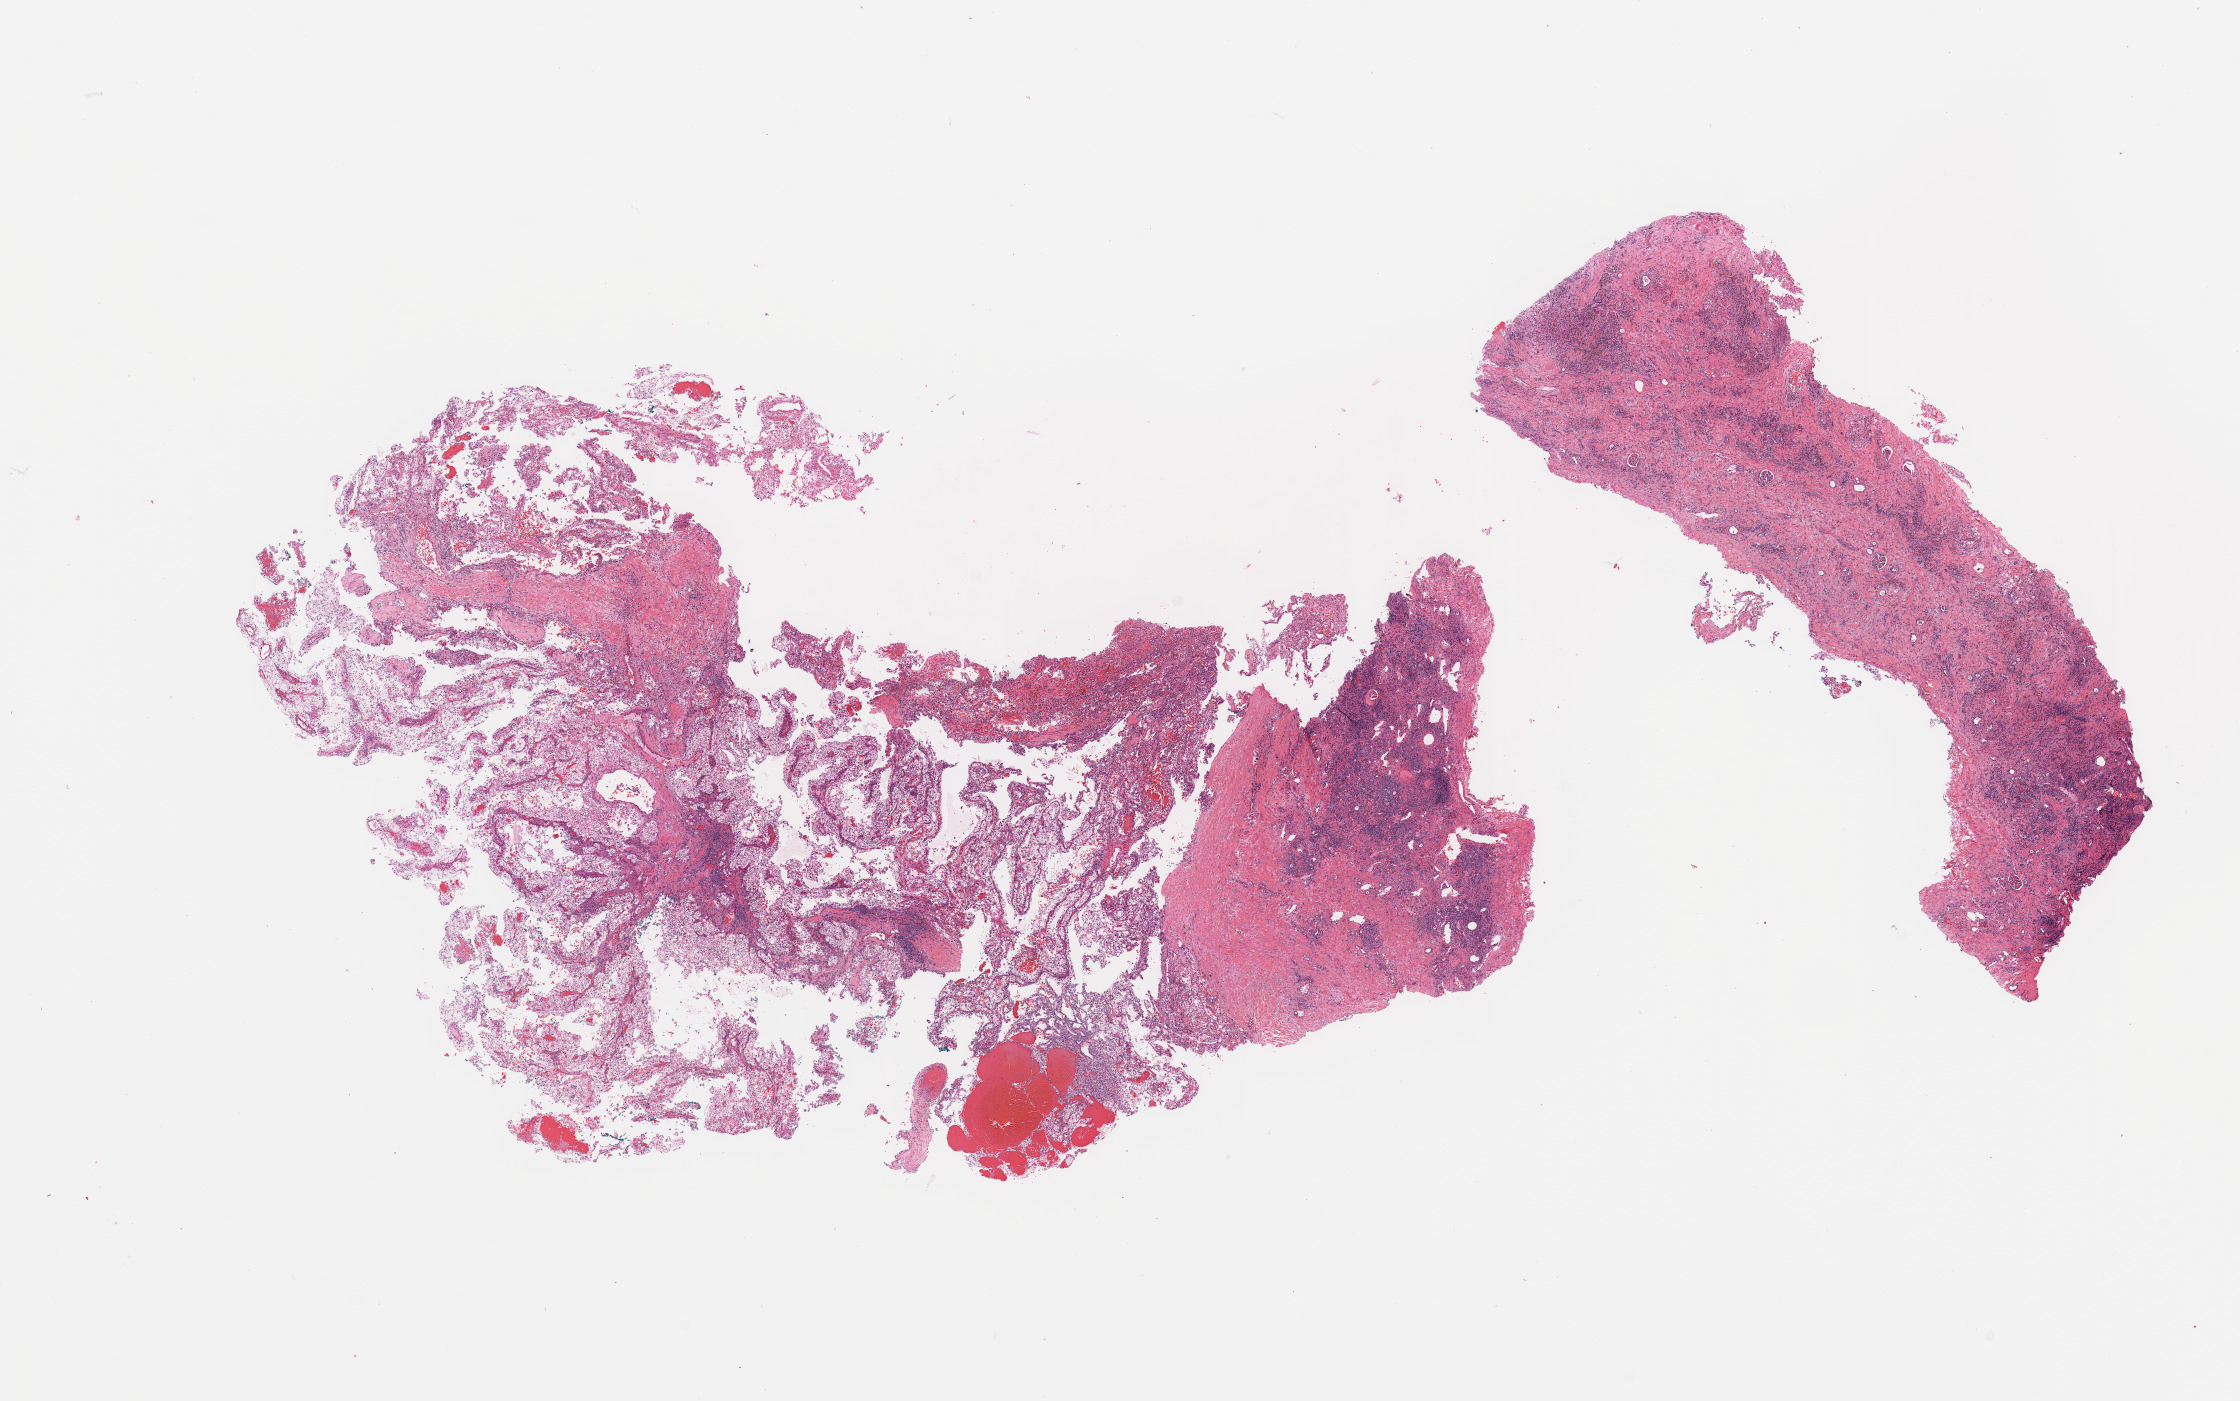
Whole-slide histology image, Hematoxylin and eosin (H&E) stained, whole scanned area (about 17.7 x 11.1 mm) shown as a low-resolution overview, kidney, tumour tissue. Patient: male, age 63 years. Histologic grade: G2 (moderately differentiated).
Diagnosis: Renal cell carcinoma, NOS. Primary tumour site (as recorded): lower pole. AJCC pathologic stage: I.